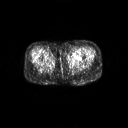
FDG PET of an extremity soft-tissue mass (from a PET/CT study), one axial slice. Position 11 of 267 along the scan axis. 128 × 128 image matrix, field of view 700 × 700 mm. Patient: female, 47 years. From the clinical record (not read from this slice): histological type: myxofibrosarcoma; grade: intermediate; site of the primary tumour: left thigh.
Annotated regions visible in this slice (expert contour drawn on MRI and transferred to this co-registered scan by the dataset authors):
- gross tumour volume including surrounding oedema: bounding box [x1, y1, x2, y2] px = [68, 53, 81, 62]